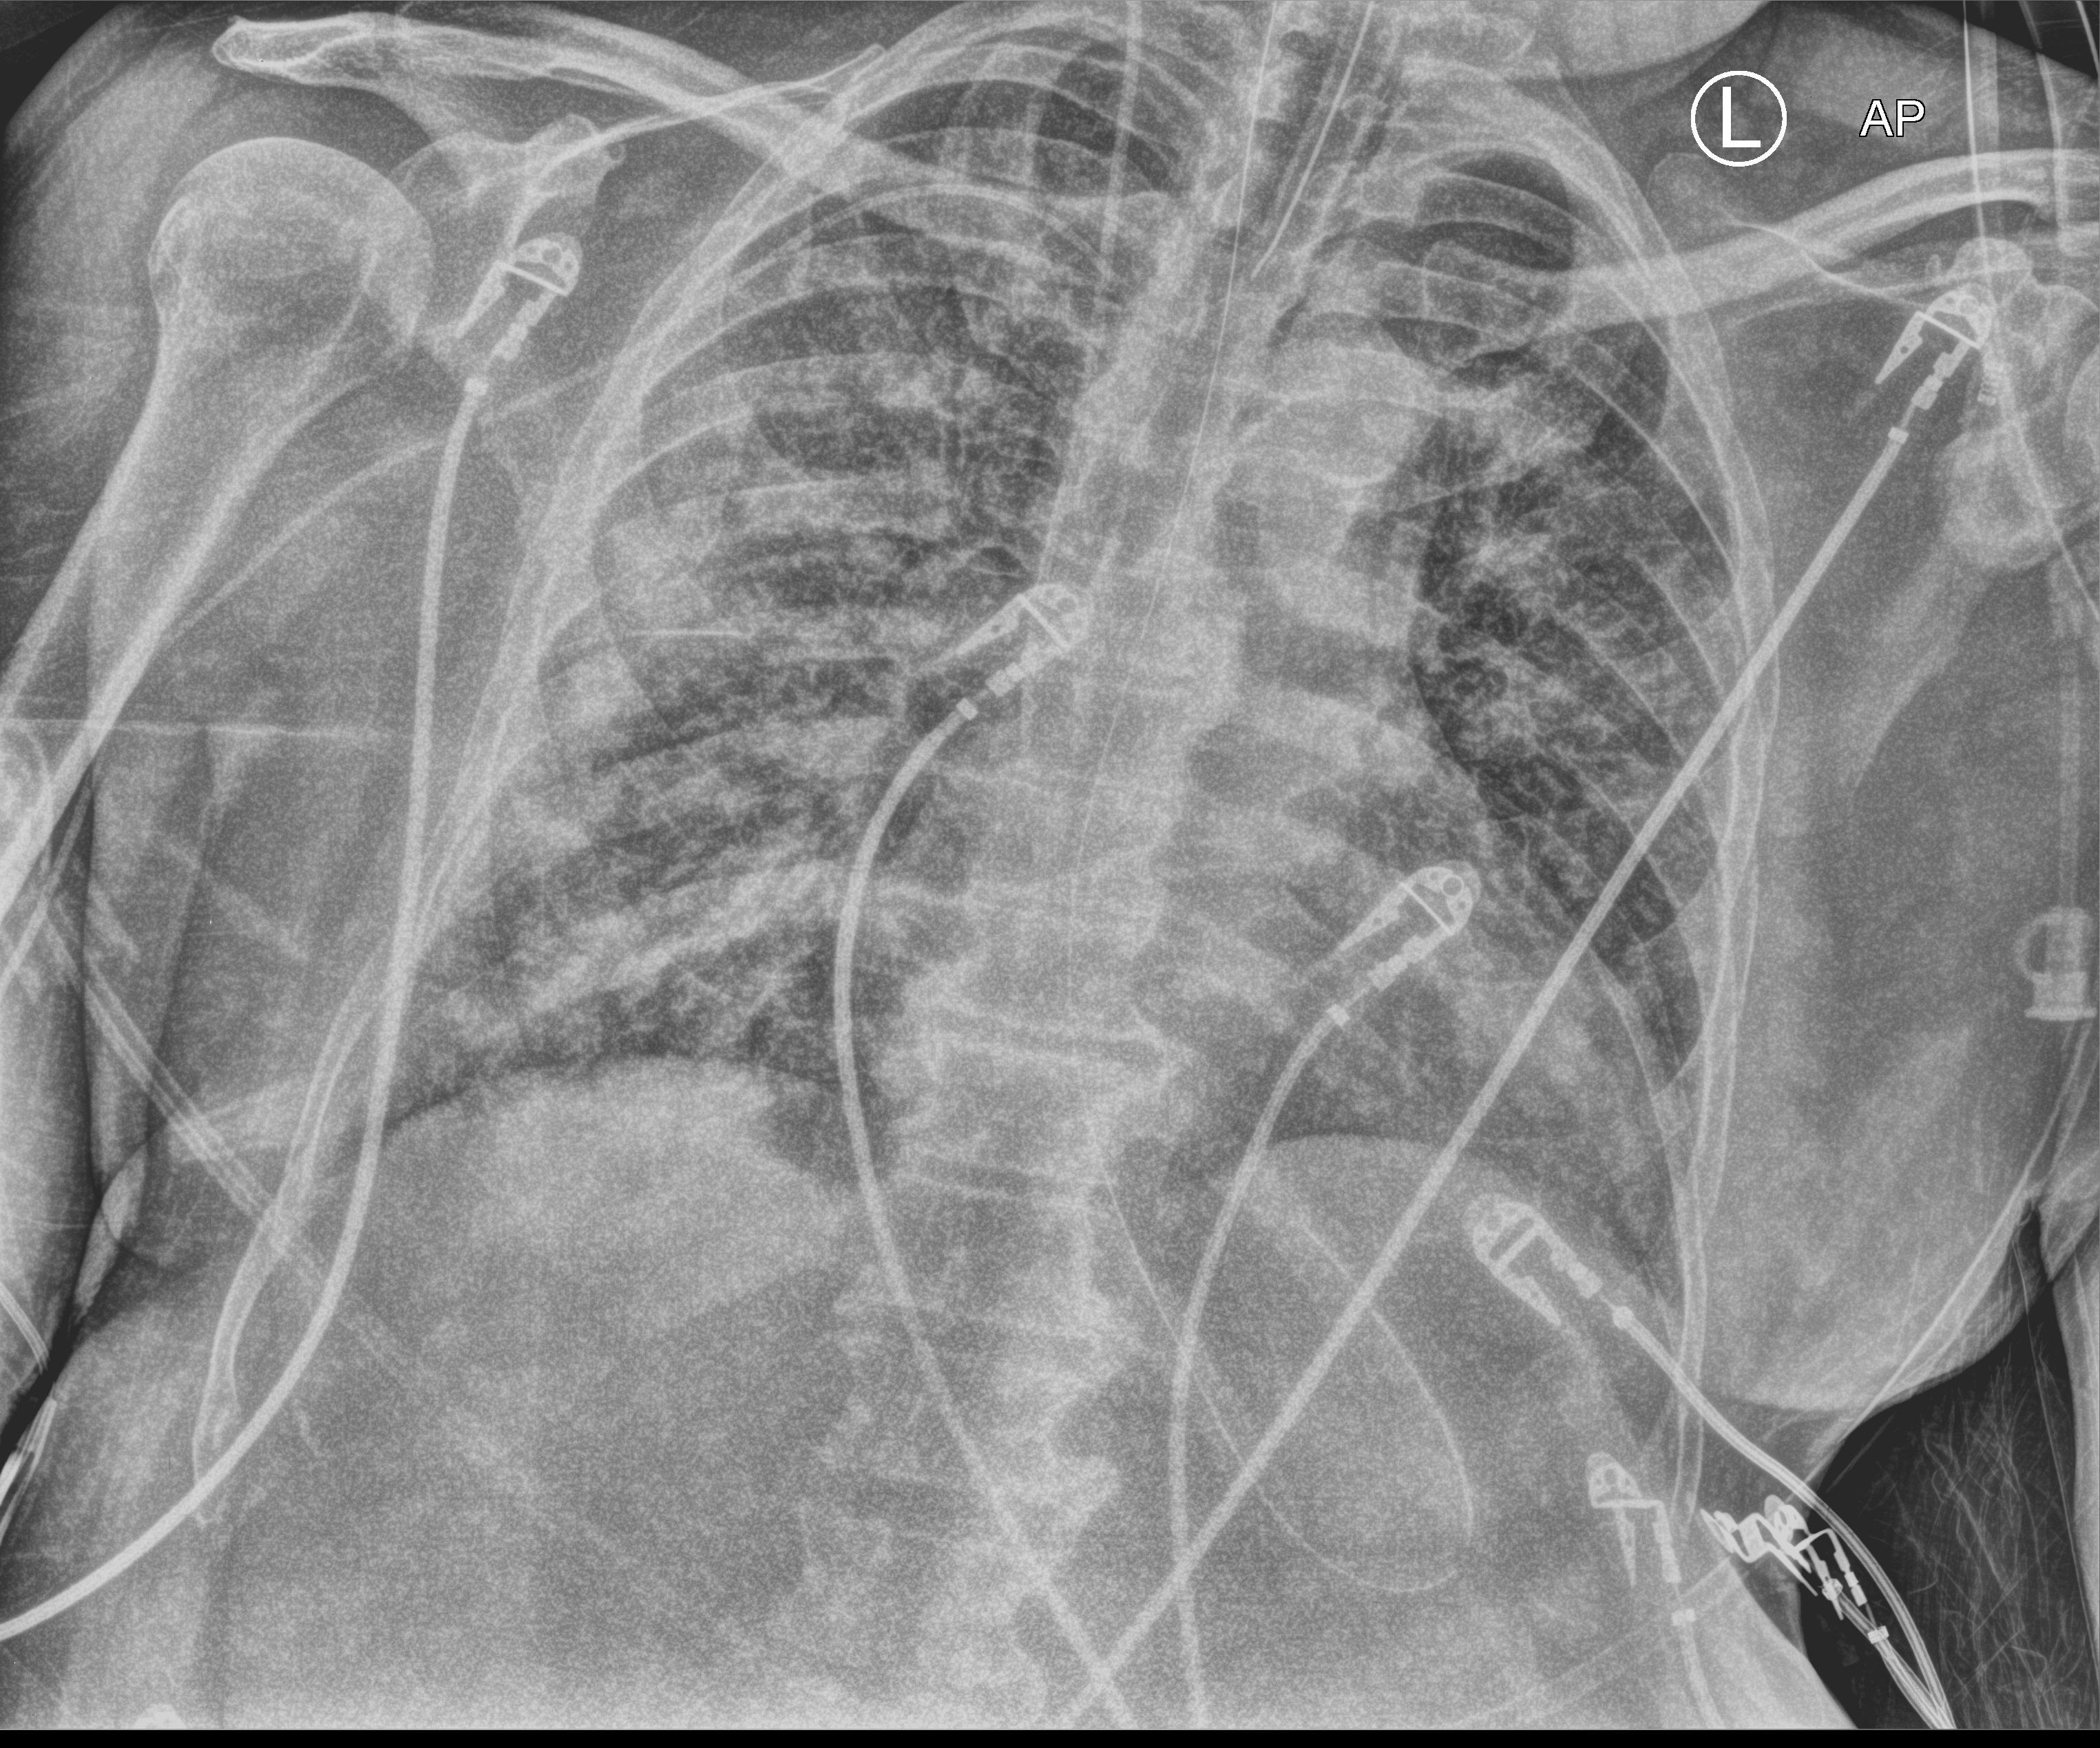
Chest X-ray (portable), anteroposterior (AP) projection. Male patient hospitalised with COVID-19, age 60–74 years.
Admission-level facts for this patient (not findings on this image; timing relative to this image not recorded): length of hospital stay: 31 days; admitted to intensive care during this hospital stay: yes; other chronic lung disease (admission record): yes.